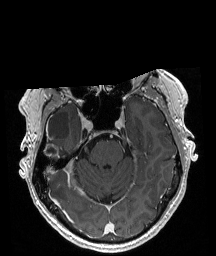
Brain MRI from a brain-tumour surgery series, one axial slice. T1-weighted post-contrast. 1 mm slice thickness. 216 × 256 image matrix, field of view 211 × 250 mm. From the clinical record (not read from this slice): histopathology: Astrocytoma; WHO grade: 4; IDH mutation: yes; tumour location: Right Temporal.
Outlined on this slice (expert manual segmentation):
- tumour: bounding box (x1, y1, x2, y2) in pixels: (45, 143, 59, 173)